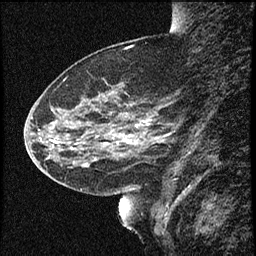
Breast MRI (dynamic contrast-enhanced), one sagittal slice; slice 21 of 60 in the series (ordered by position); dynamic contrast-enhanced study with each time point stored as its own series, time point 2 of 4 at this slice position (early post-contrast, ordered by acquisition time); 1.5 T; TE 4.2 ms, TR 16.7 ms; 2 mm slice thickness; 256 × 256 image matrix, field of view 200 × 200 mm. Female patient, age 52 years. Case-level facts recorded for this patient, not image findings: setting: breast cancer imaged before/during neoadjuvant chemotherapy; receptor status: HER2-positive.
Structures marked on this image (semi-automatically segmented with operator editing):
- analysis volume of interest (the breast-tissue region the enhancement analysis was run in; not a lesion): box from (x=37, y=79) to (x=165, y=181) px
- tumour enhancement mask (voxels above the 100 % enhancement threshold inside the analysis volume of interest): (x=85, y=163)–(x=87, y=165)